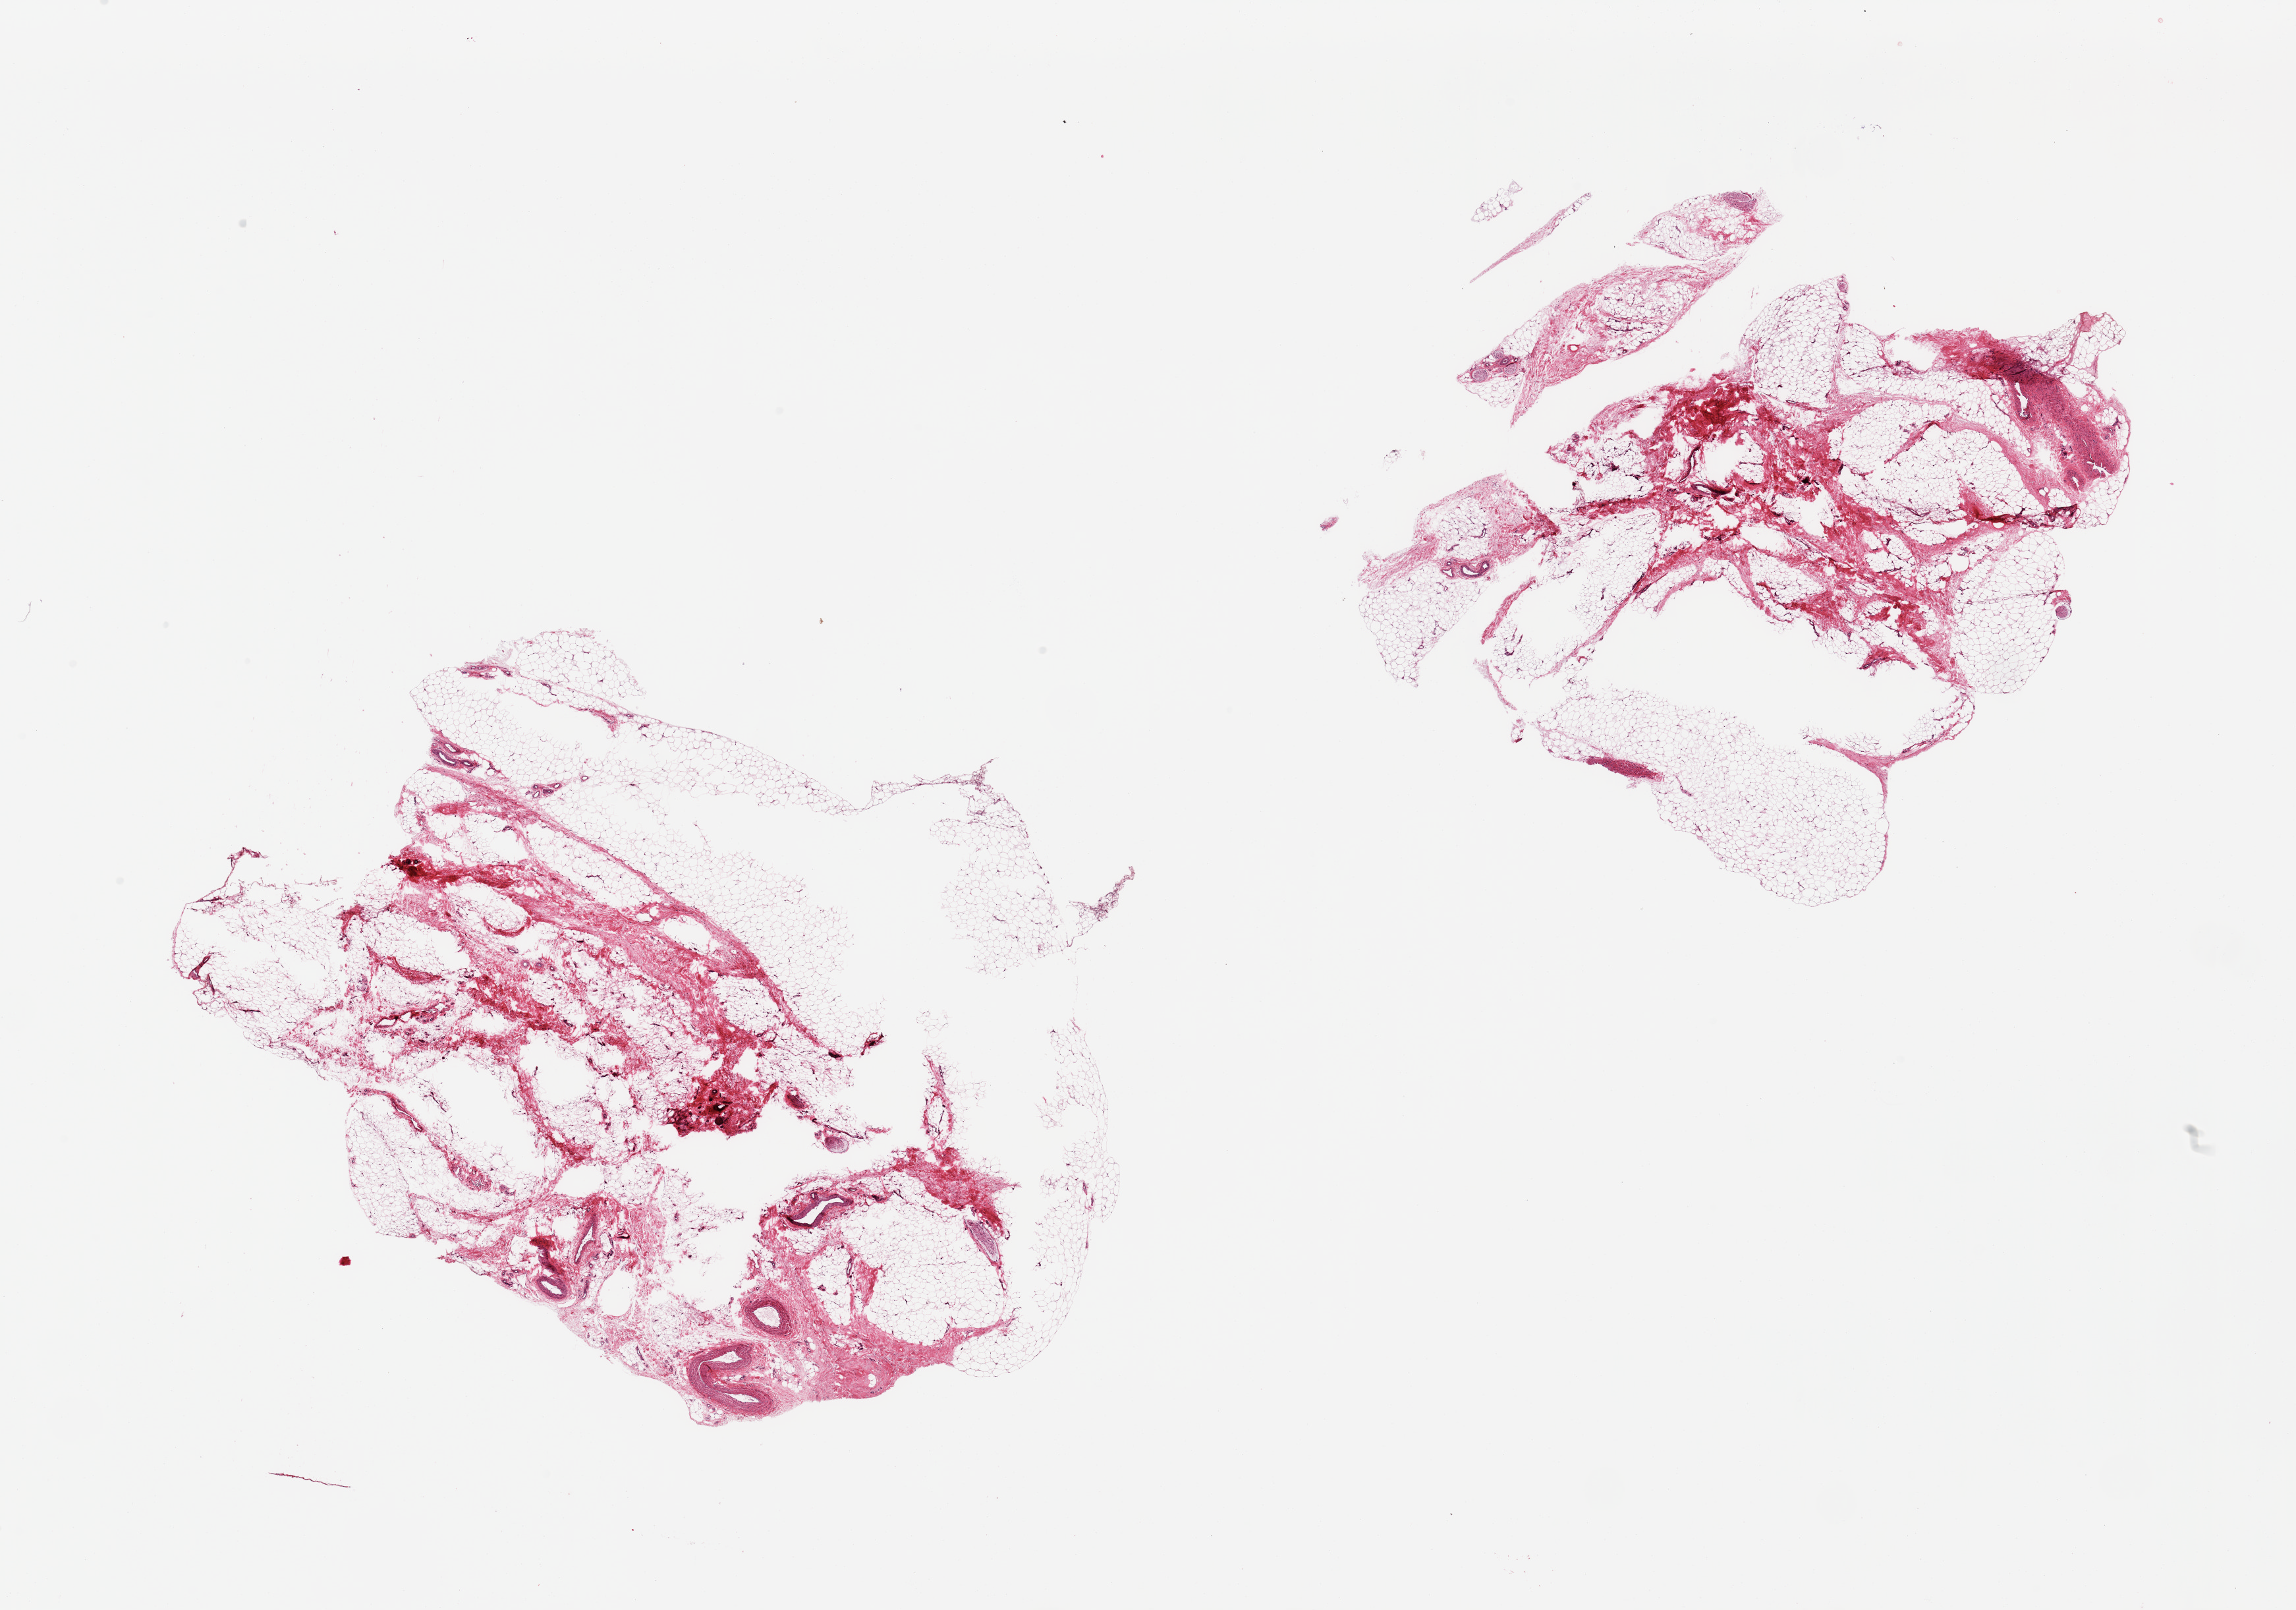
Hematoxylin and eosin (H&E) whole-slide image, whole scanned area (about 27.6 x 19.3 mm, acquisition: 20x scan) shown as a low-resolution overview; PAXgene-fixed paraffin-embedded (PFPE) section; section of adipose tissue (target tissue); donor tissue sample. Male donor.
Reviewer comment on this tissue sample: 2 pieces, ~50% fascia/vascular elements; Sample with caution.